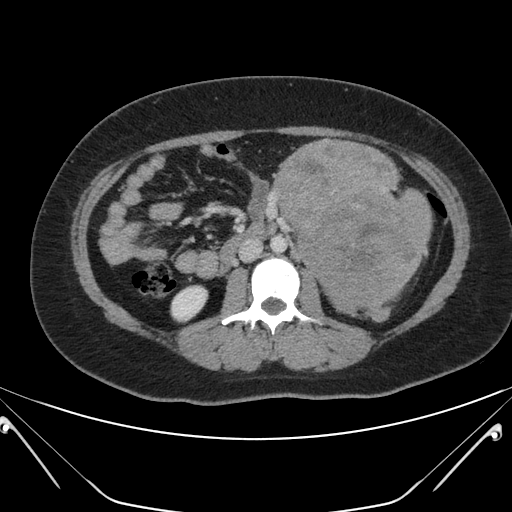
Contrast-enhanced abdominal CT, one axial slice; position 100 of 168 along the scan axis; 120 kVp; intravenous contrast given; soft-tissue window (W 400 / L 40 HU); 3 mm slice thickness; 512 × 512 image matrix. Female patient, age 26 years. From the clinical record (not read from this slice): diagnosis: adrenocortical carcinoma; tumour side: left adrenal; tumour size at pathology: 28 cm; Ki-67 index: 20 %; stage (as recorded): 2.
Structures marked on this image (semi-automatic segmentation, software-assisted and operator-edited):
- mass: box from (x=276, y=138) to (x=431, y=320) px